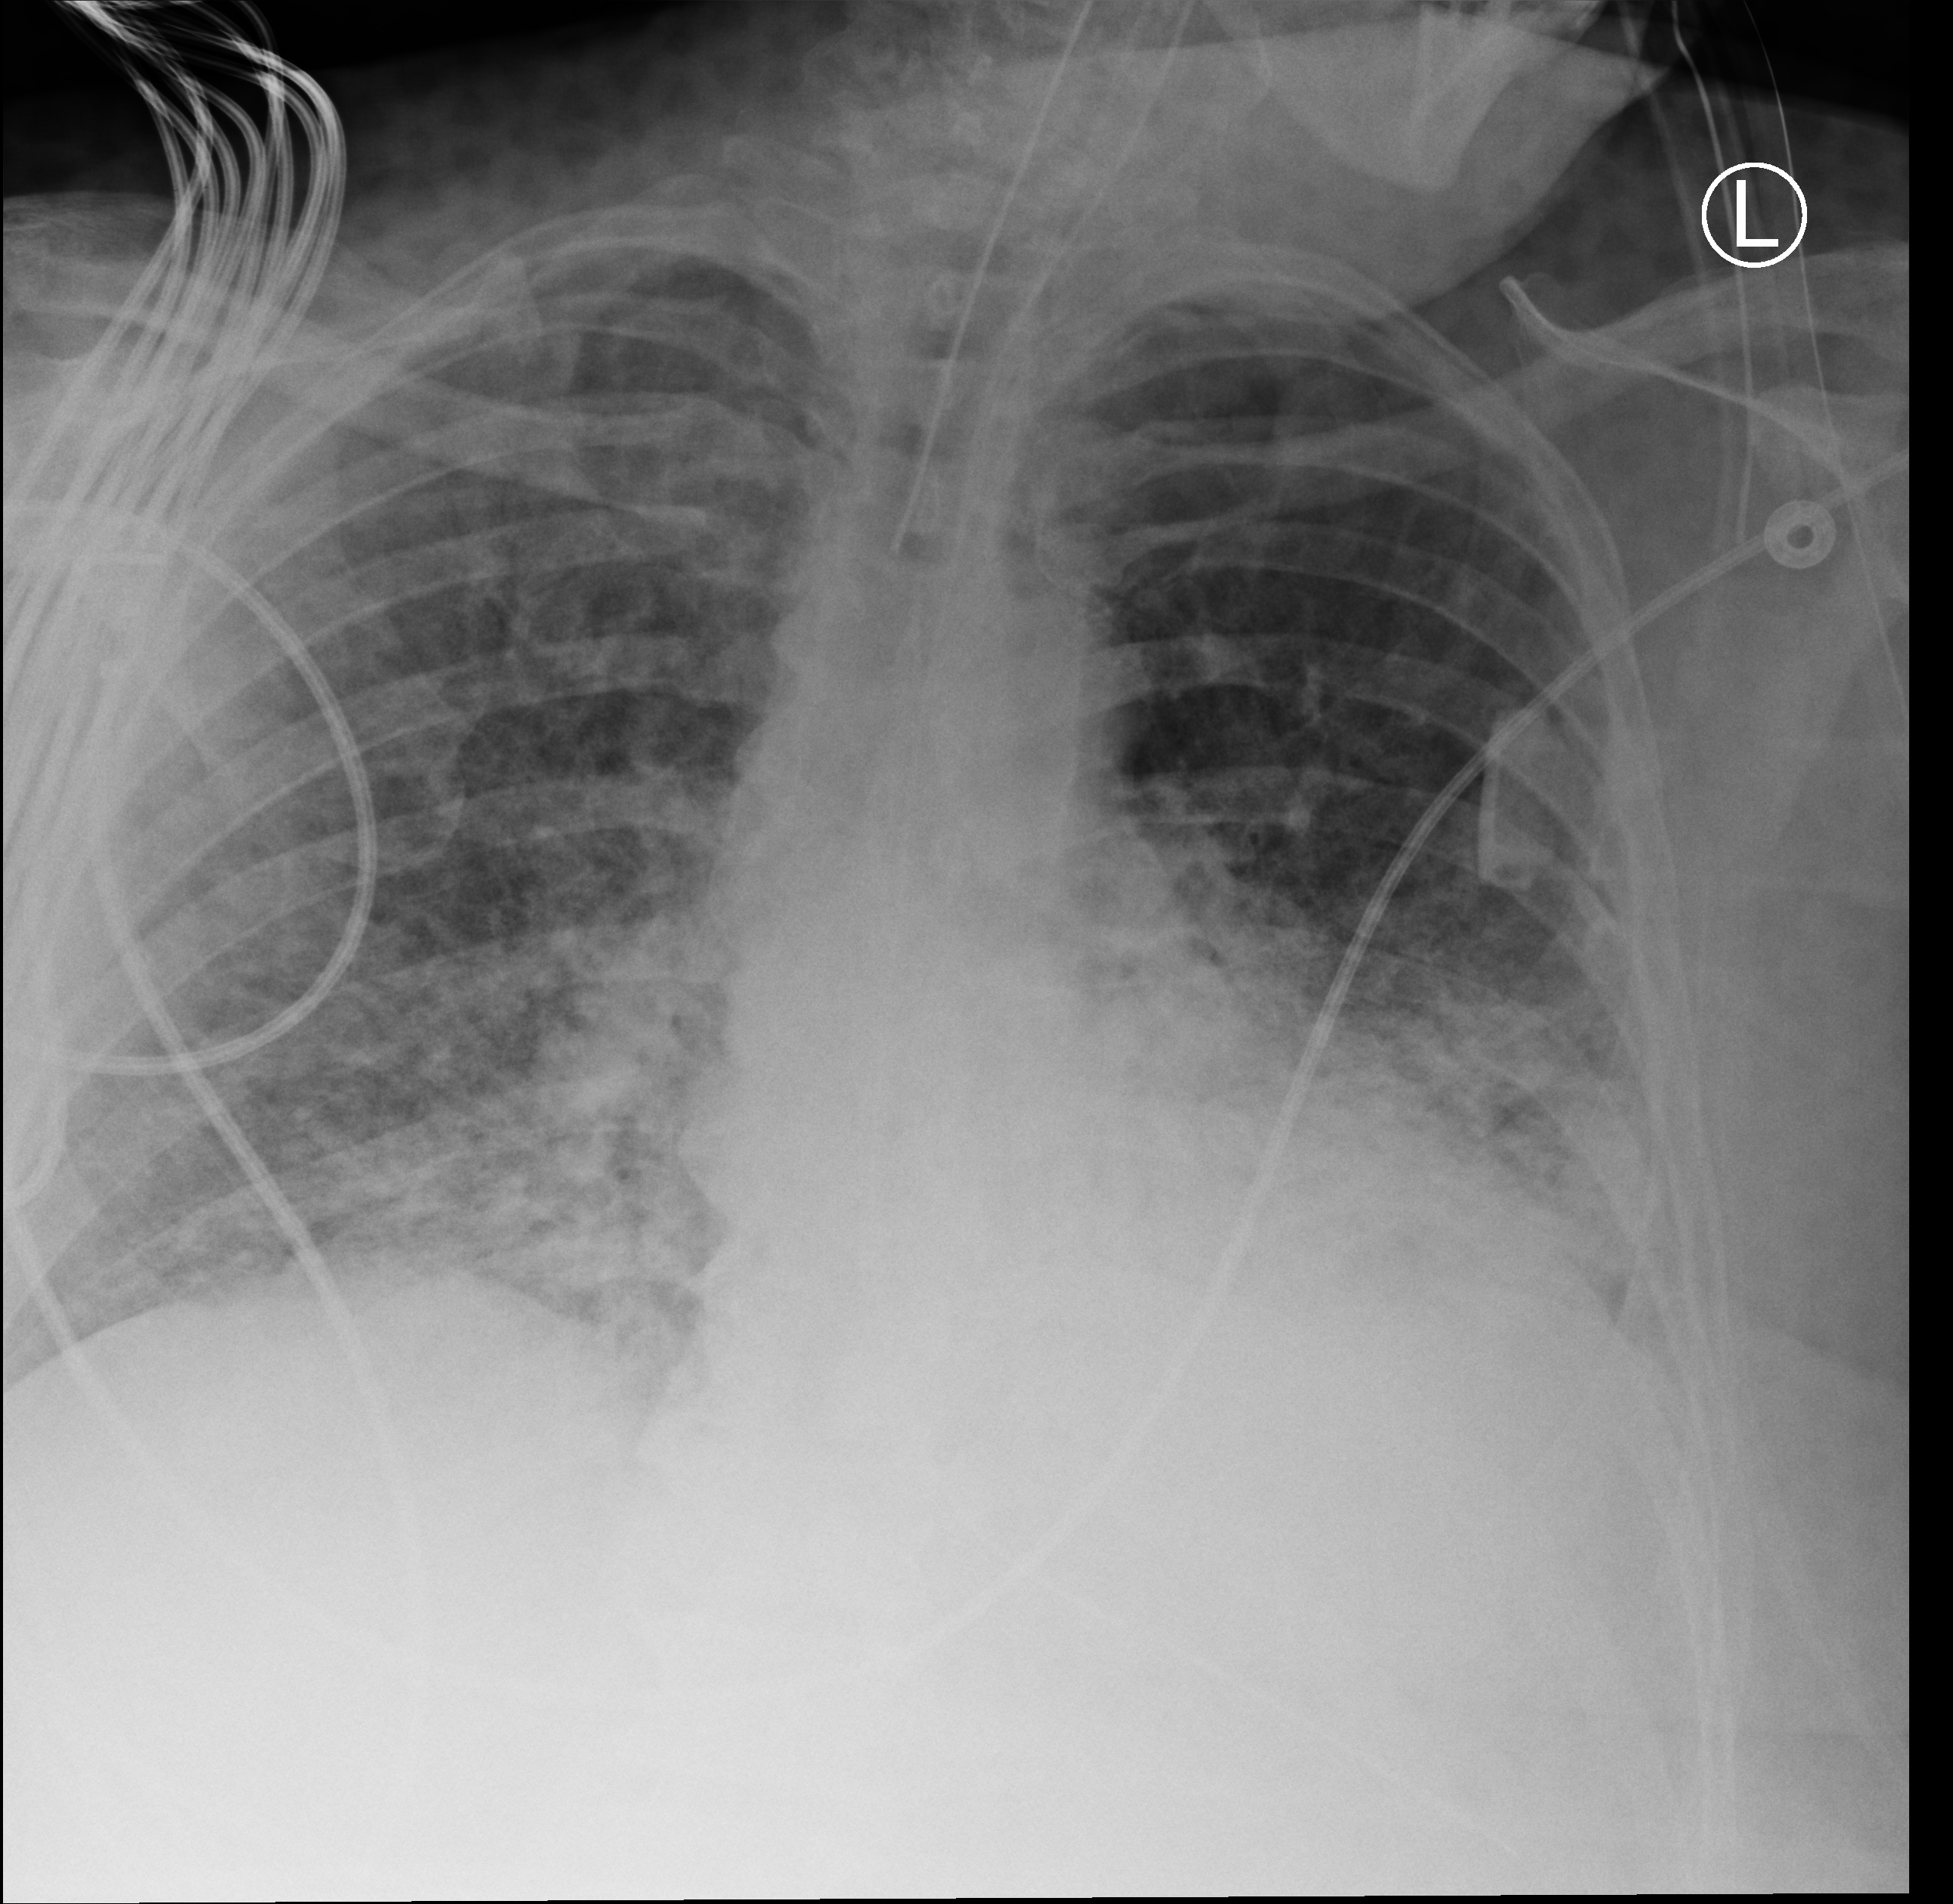
Chest X-ray (portable); anteroposterior (AP) projection. Patient hospitalised with COVID-19, aged 18–59 years.
Hospital-stay facts (about this admission, not read from this image; timing relative to this image not recorded):
- mechanically ventilated during this hospital stay: yes